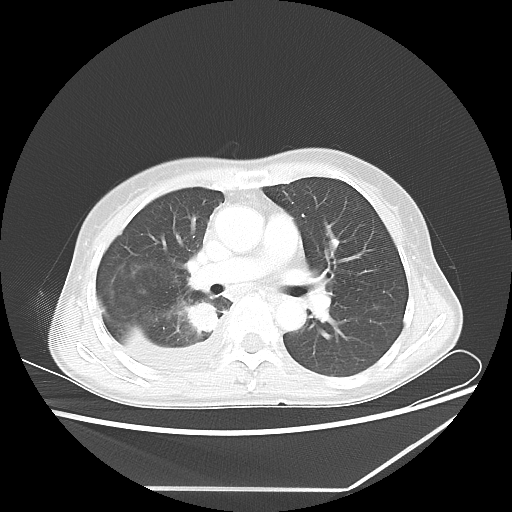
Chest CT, one axial slice; position 35 of 60 along the scan axis; reconstruction kernel LUNG; 80 kVp; lung window (W 1500 / L -600 HU); 5 mm slice thickness; 512 × 512 image matrix, field of view 364 × 364 mm. Female patient, age 59 years. From the clinical record (not read from this slice): clinical TNM (as recorded): T1c N1 M1.
Annotated regions visible in this slice (bounding box drawn by a radiologist):
- lung tumour (recorded histology: adenocarcinoma): bounding box (x1, y1, x2, y2) in pixels: (182, 298, 219, 335)